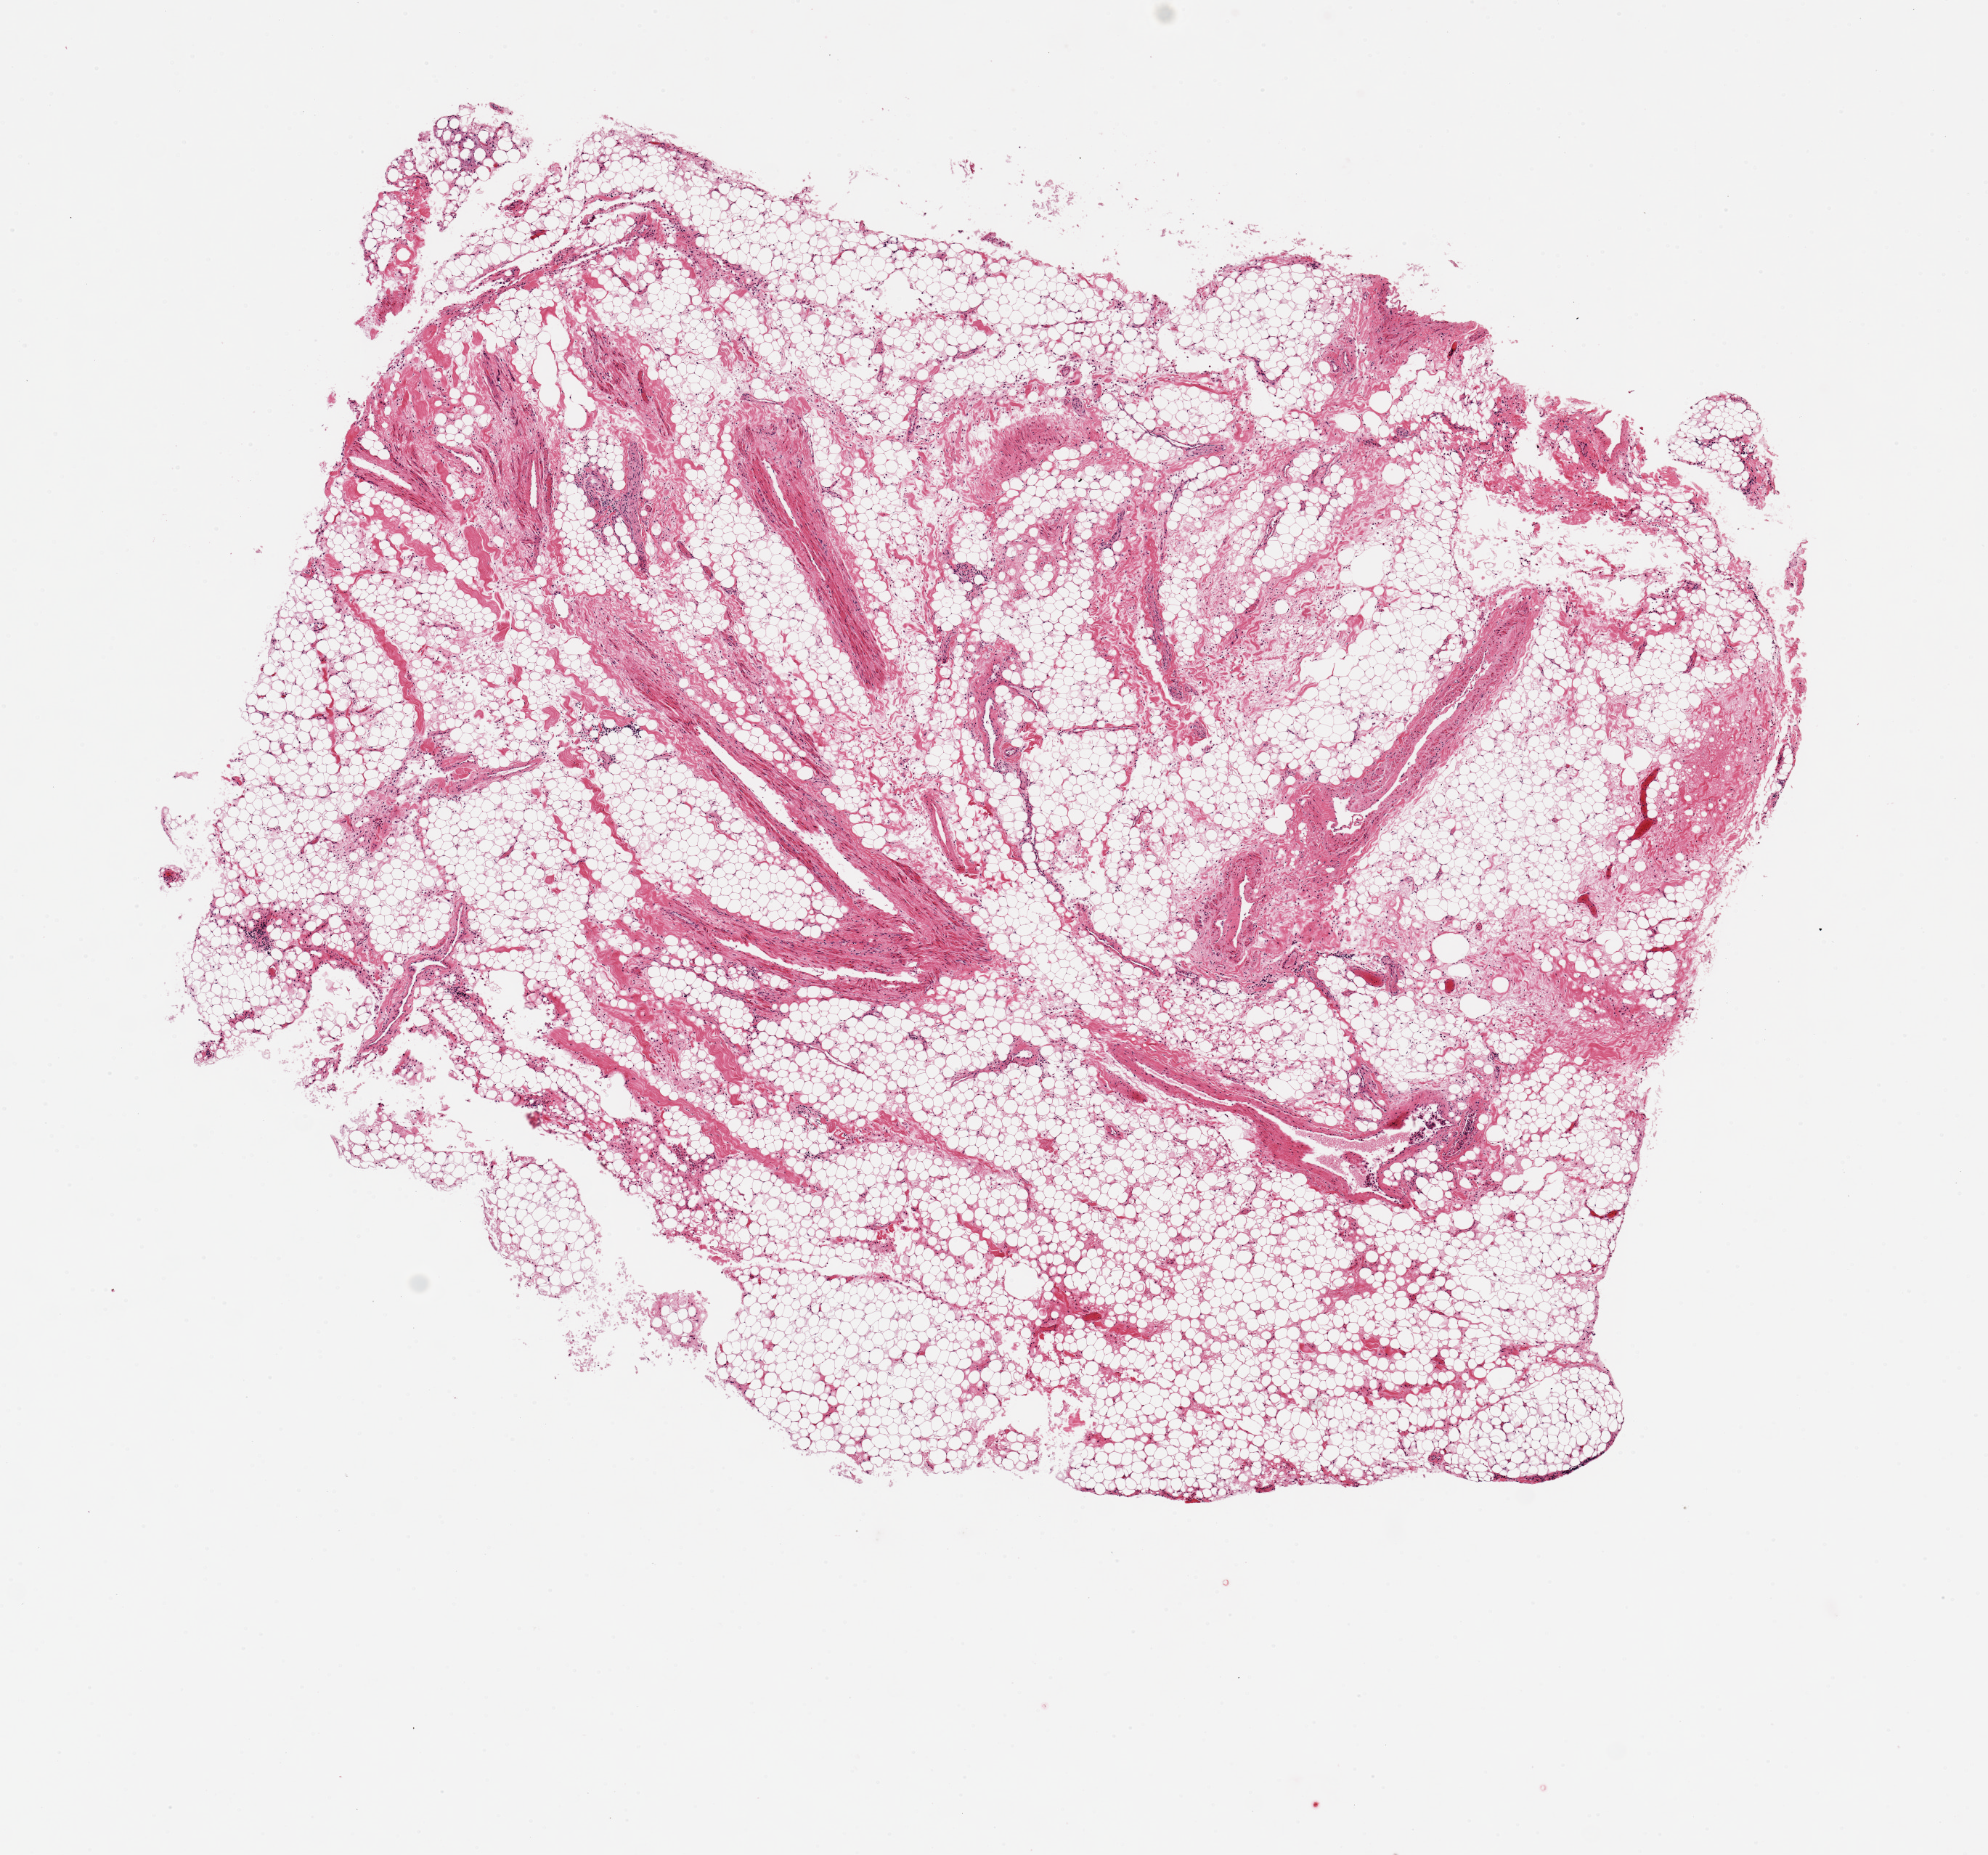
H&E whole-slide image — shown as a low-resolution overview of the whole scanned area (about 10.8 x 10.1 mm); PAXgene-fixed, paraffin-embedded tissue; section of auricular appendage (target tissue); donor tissue sample. Donor sex: male.
* pathologist's review note for this sample: 1 piece, ~8x6mm unususually badly autolyzed